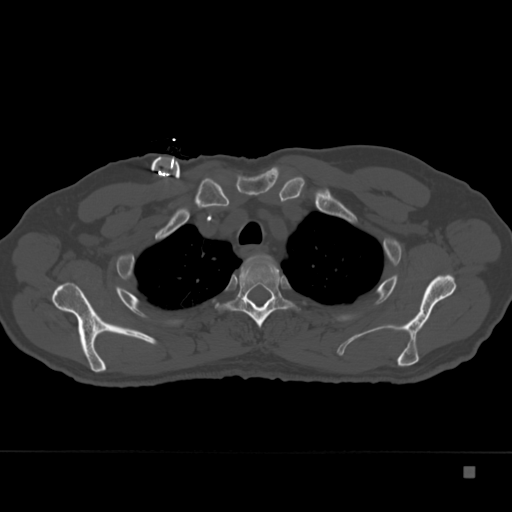
CT including the spine, one axial slice. Position 288 of 332 along the scan axis. Reconstruction kernel Br40s. Bone window (W 1800 / L 400 HU). 1.5 mm slice thickness. 512 × 512 image matrix. Patient: male, 72 years. From the clinical record (not read from this slice): primary cancer: skeletal.
Structures marked on this image (semi-automatically segmented with operator editing):
- T2 vertebra: bounding box (x1, y1, x2, y2) in pixels: (232, 274, 237, 278)
- T3 vertebra: (216, 256, 295, 328)